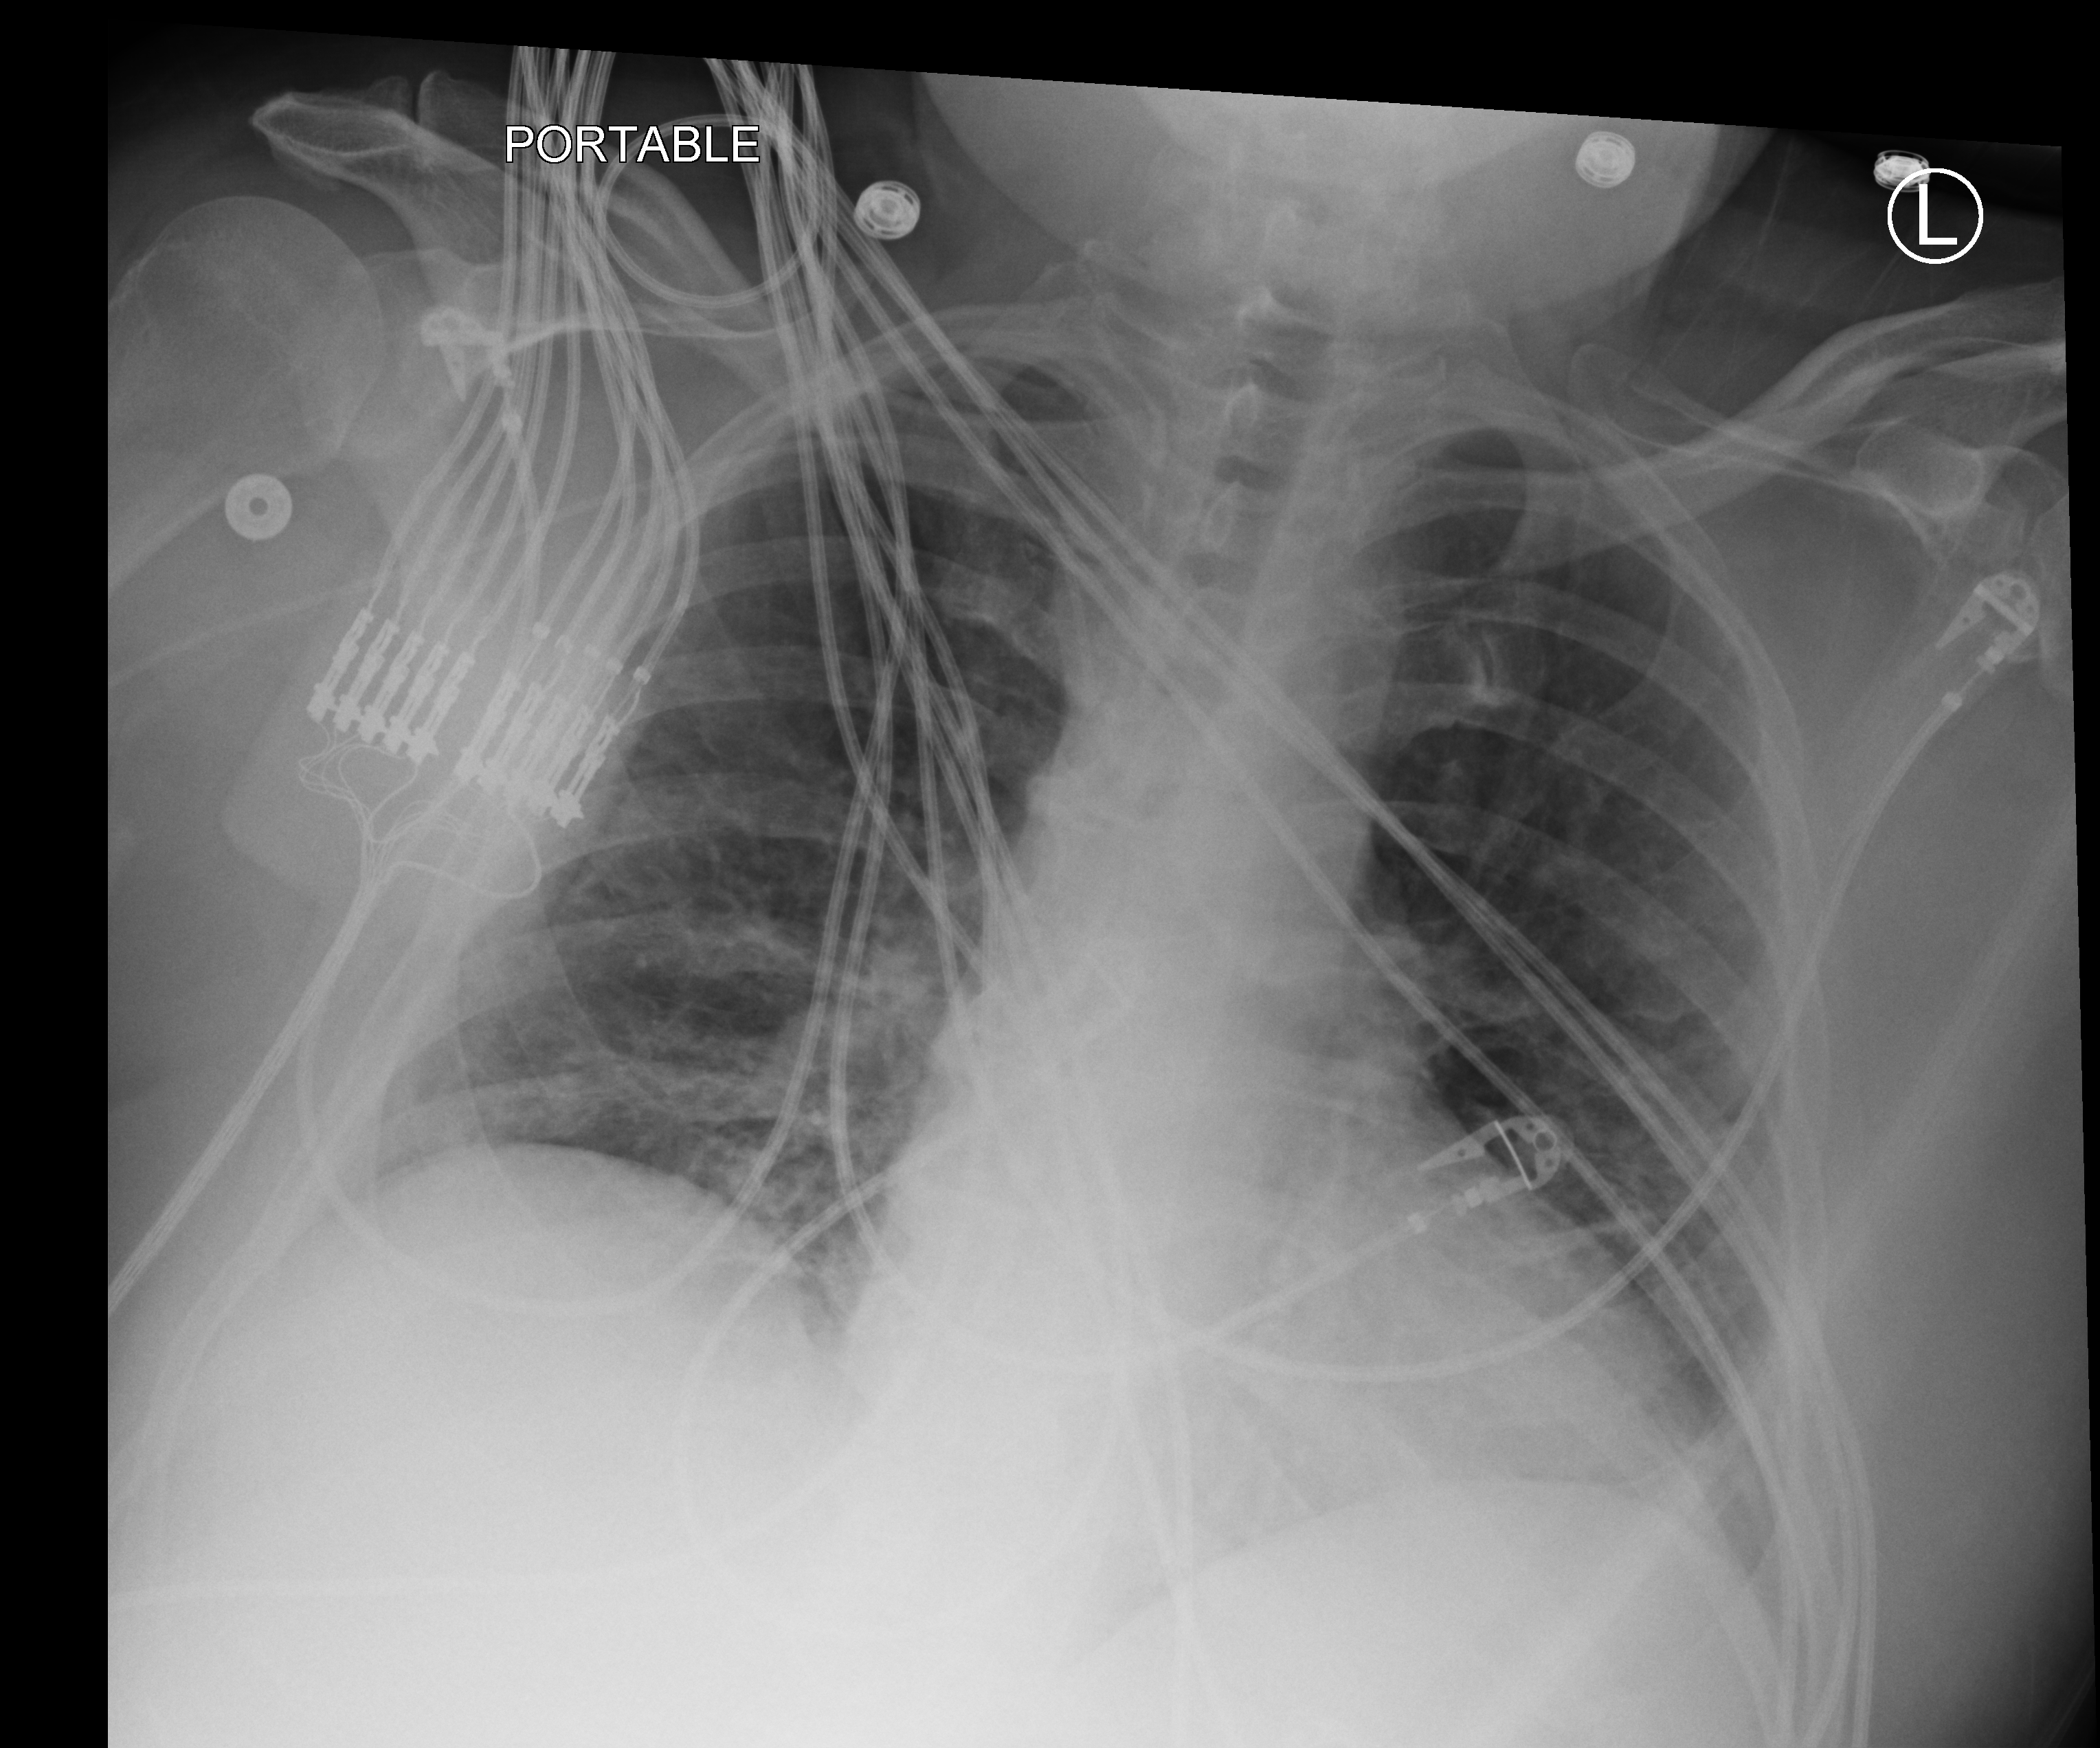
Chest X-ray (portable); anteroposterior (AP) projection. Patient hospitalised with COVID-19; male, aged 18–59 years.
Admission-level facts for this patient (not findings on this image; timing relative to this image not recorded):
- diabetes (admission record): no
- hypertension (admission record): yes